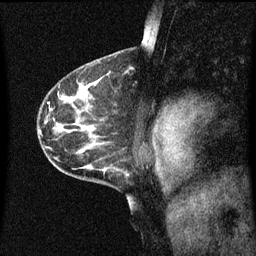
Breast MRI (dynamic contrast-enhanced), one sagittal slice; position 39 of 60 along the scan axis; dynamic contrast-enhanced series, image 2 of 3 at this slice position (ordered by acquisition); 1.5 T; TE 4.2 ms, TR 8.4 ms; 2 mm slice thickness; 256 × 256 image matrix, field of view 200 × 200 mm. Female patient, age 41 years.
Annotated regions visible in this slice (semi-automatically segmented with operator editing):
- analysis volume of interest (the breast-tissue region the enhancement analysis was run in; not a lesion): bounding box [x1, y1, x2, y2] px = [121, 60, 136, 81]
- tumour enhancement mask (voxels above the 70 % enhancement threshold inside the analysis volume of interest): [129, 68, 135, 71]